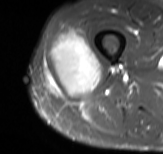
MRI of an extremity soft-tissue mass, one axial slice; position 31 of 61 along the scan axis; STIR; MR volume resampled by the dataset authors to the PET/CT grid (not the native acquisition matrix); 163 × 154 image matrix, field of view 159 × 150 mm. Male patient. Case-level facts recorded for this patient, not image findings: histological type: poorly differentiated synovial sarcoma; grade: high; site of the primary tumour: right buttock.
Outlined on this slice (expert contour drawn on MRI and transferred to this co-registered scan by the dataset authors):
- gross tumour volume including surrounding oedema: bounding box <48,25,102,95> (left, top, right, bottom; pixels)
- gross tumour volume (mass): <52,34,102,95>